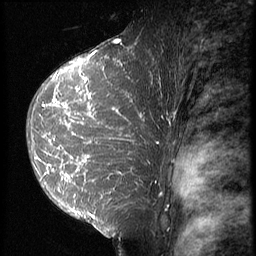
Breast MRI (dynamic contrast-enhanced), one sagittal slice; position 40 of 64 along the scan axis; 3 images stored at this slice position (order not interpretable as contrast timing); 1.5 T; TE 4.2 ms, TR 9 ms; 2.5 mm slice thickness; 256 × 256 image matrix. Female patient, age 39 years. Case-level facts recorded for this patient, not image findings: setting: breast cancer imaged before/during neoadjuvant chemotherapy; receptor status: HER2-positive.
Structures marked on this image (semi-automatically segmented with operator editing):
- analysis volume of interest (the breast-tissue region the enhancement analysis was run in; not a lesion): bounding box <26,47,155,239> (left, top, right, bottom; pixels)
- tumour enhancement mask (voxels above the 140 % enhancement threshold inside the analysis volume of interest): <38,47,152,219>